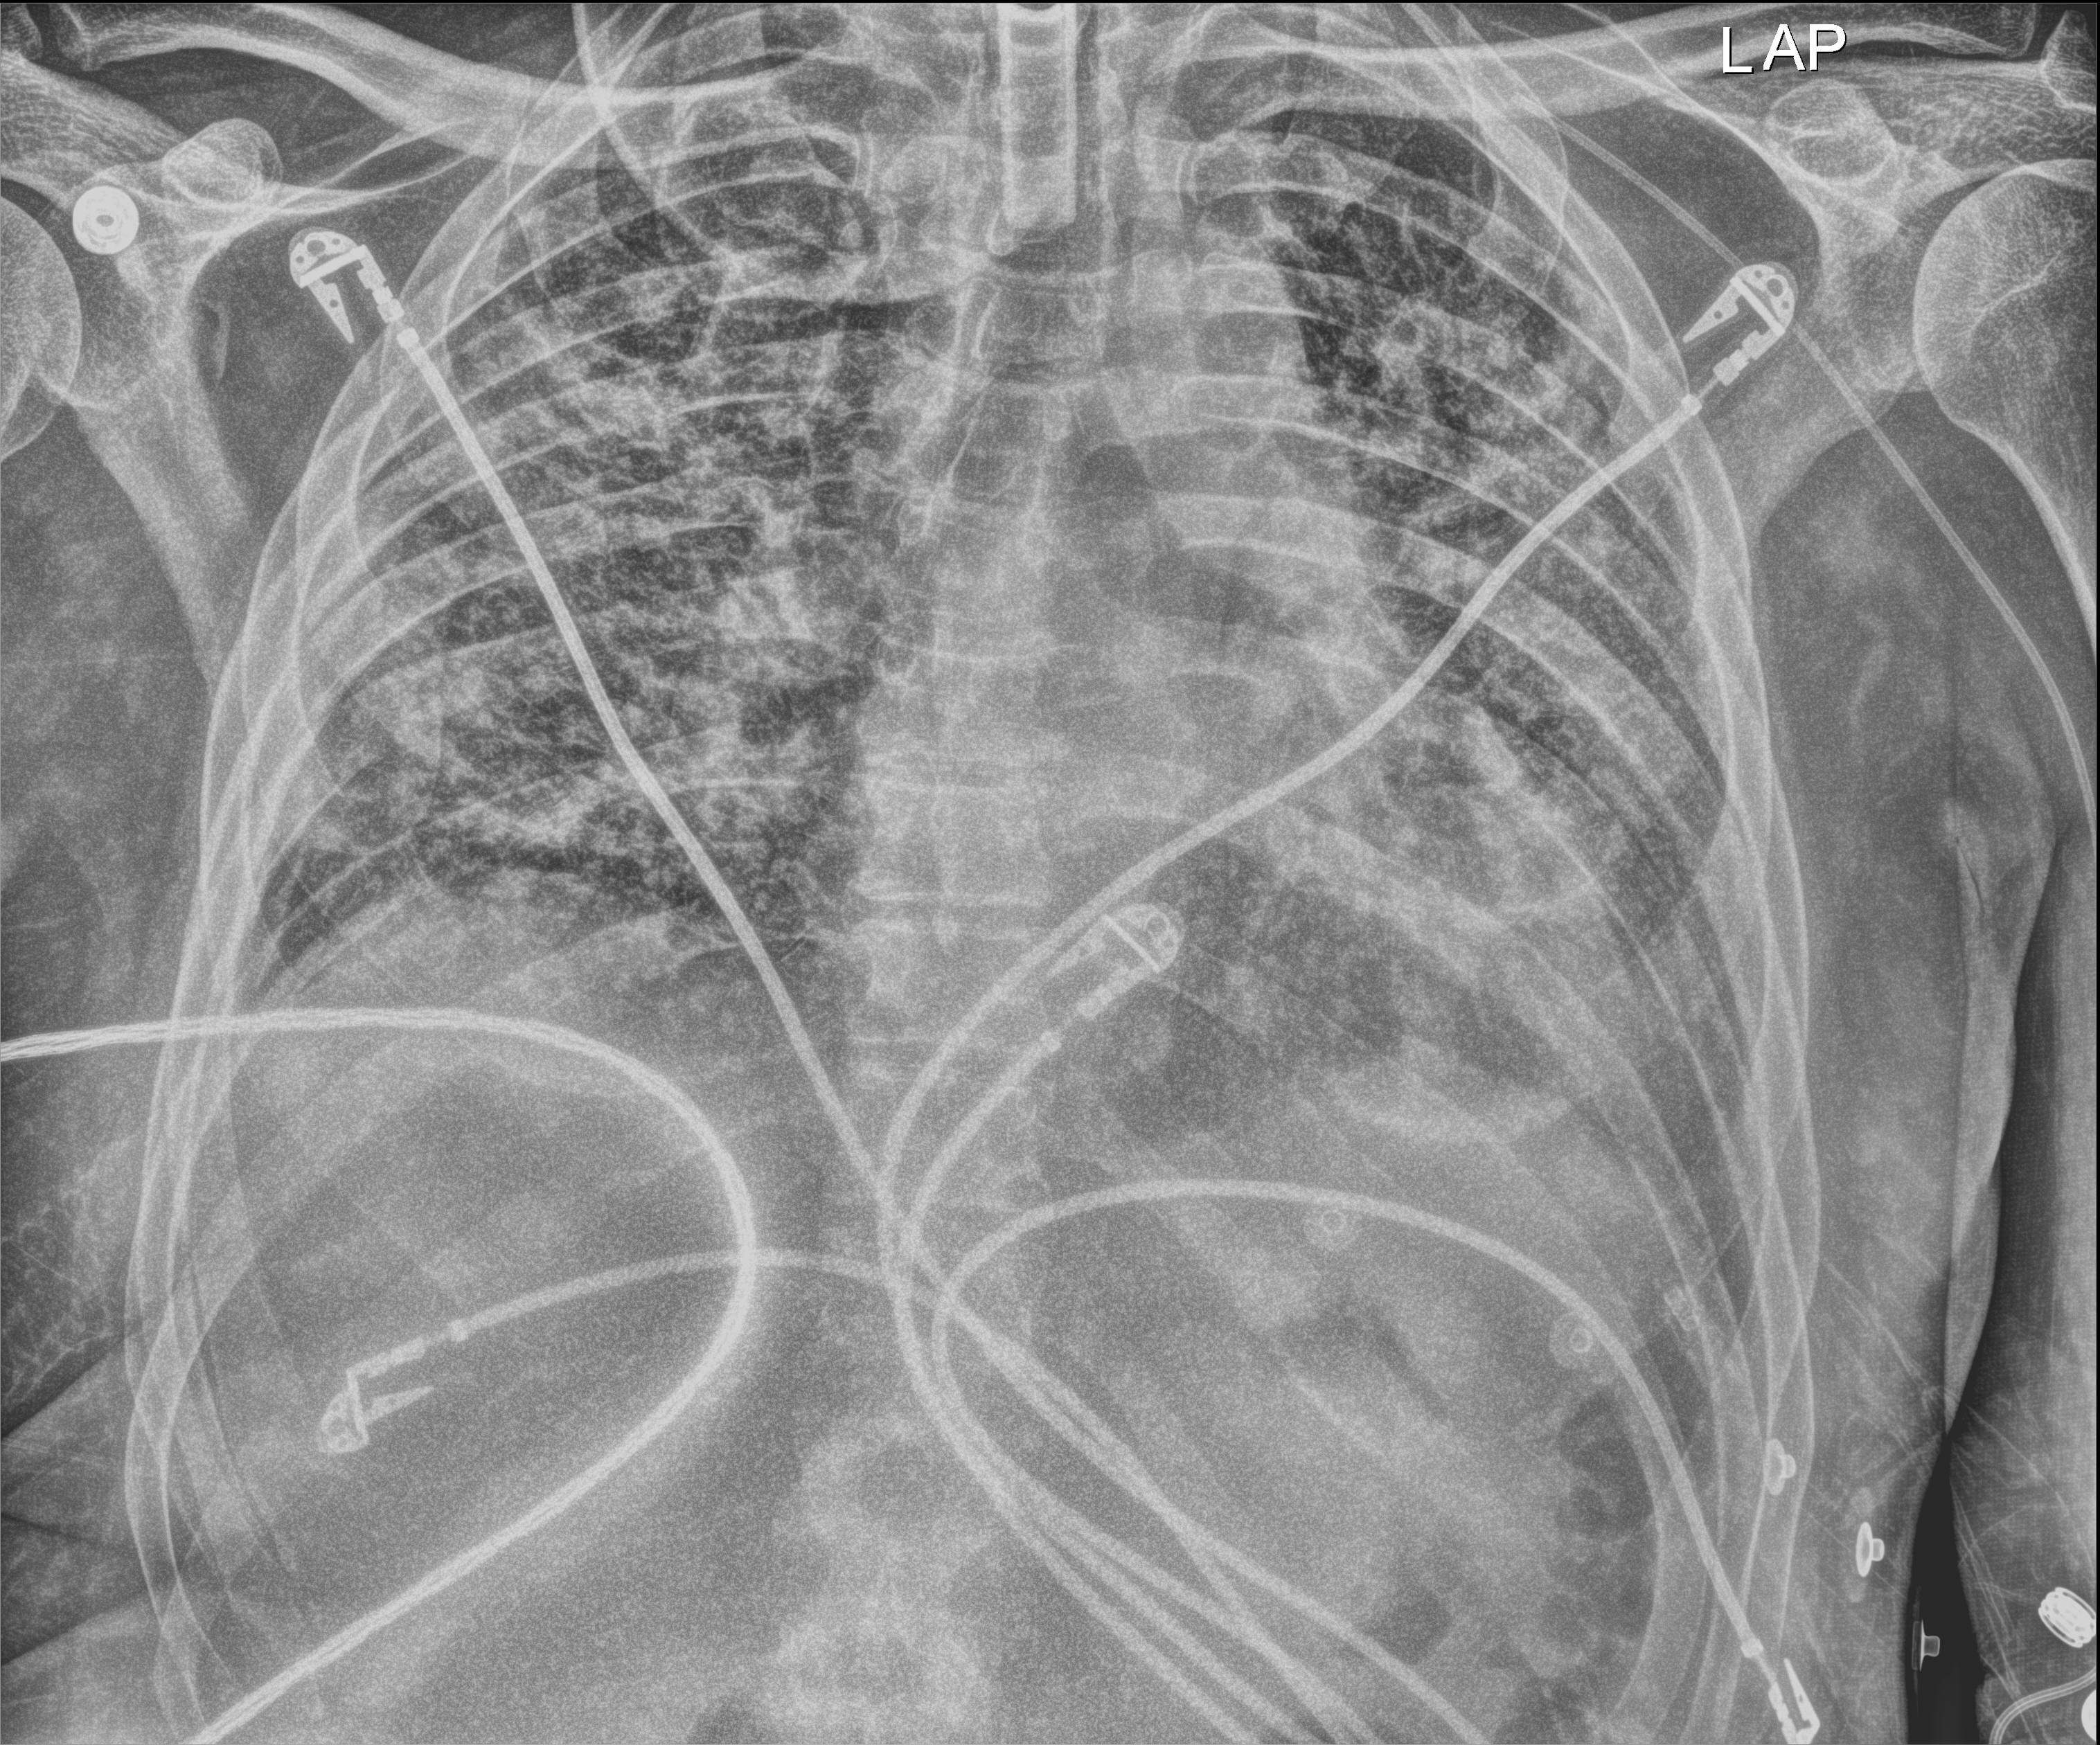
Bedside chest radiograph (digital radiography). Patient hospitalised with COVID-19; male, aged 18–59 years.
From the hospital-stay record, not from the radiograph (when in the stay this image was taken is not recorded): length of hospital stay: 75 days.